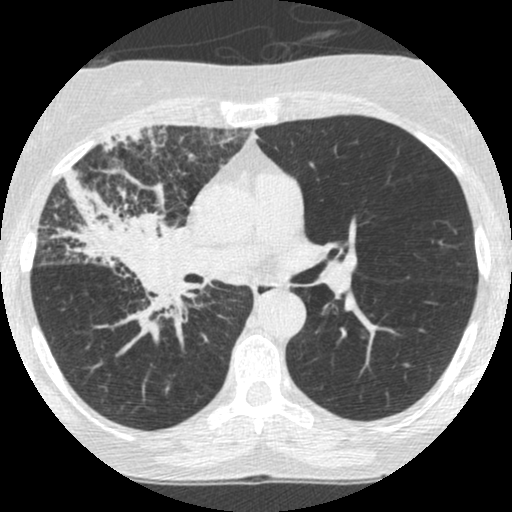
Low-dose screening chest CT, one axial slice; slice 147 of 253 in the series (ordered by position); reconstruction kernel STANDARD; lung window (W 1500 / L -600 HU); 1.25 mm slice thickness; 512 × 512 image matrix, field of view 294 × 294 mm.
Structures marked on this image (expert manual segmentation):
- lesion 2 (tumor, hilum of right lung): bounding box [x1, y1, x2, y2] px = [50, 169, 186, 342]
- lesion 3 (tumor, upper lobe of right lung): [100, 126, 170, 154]